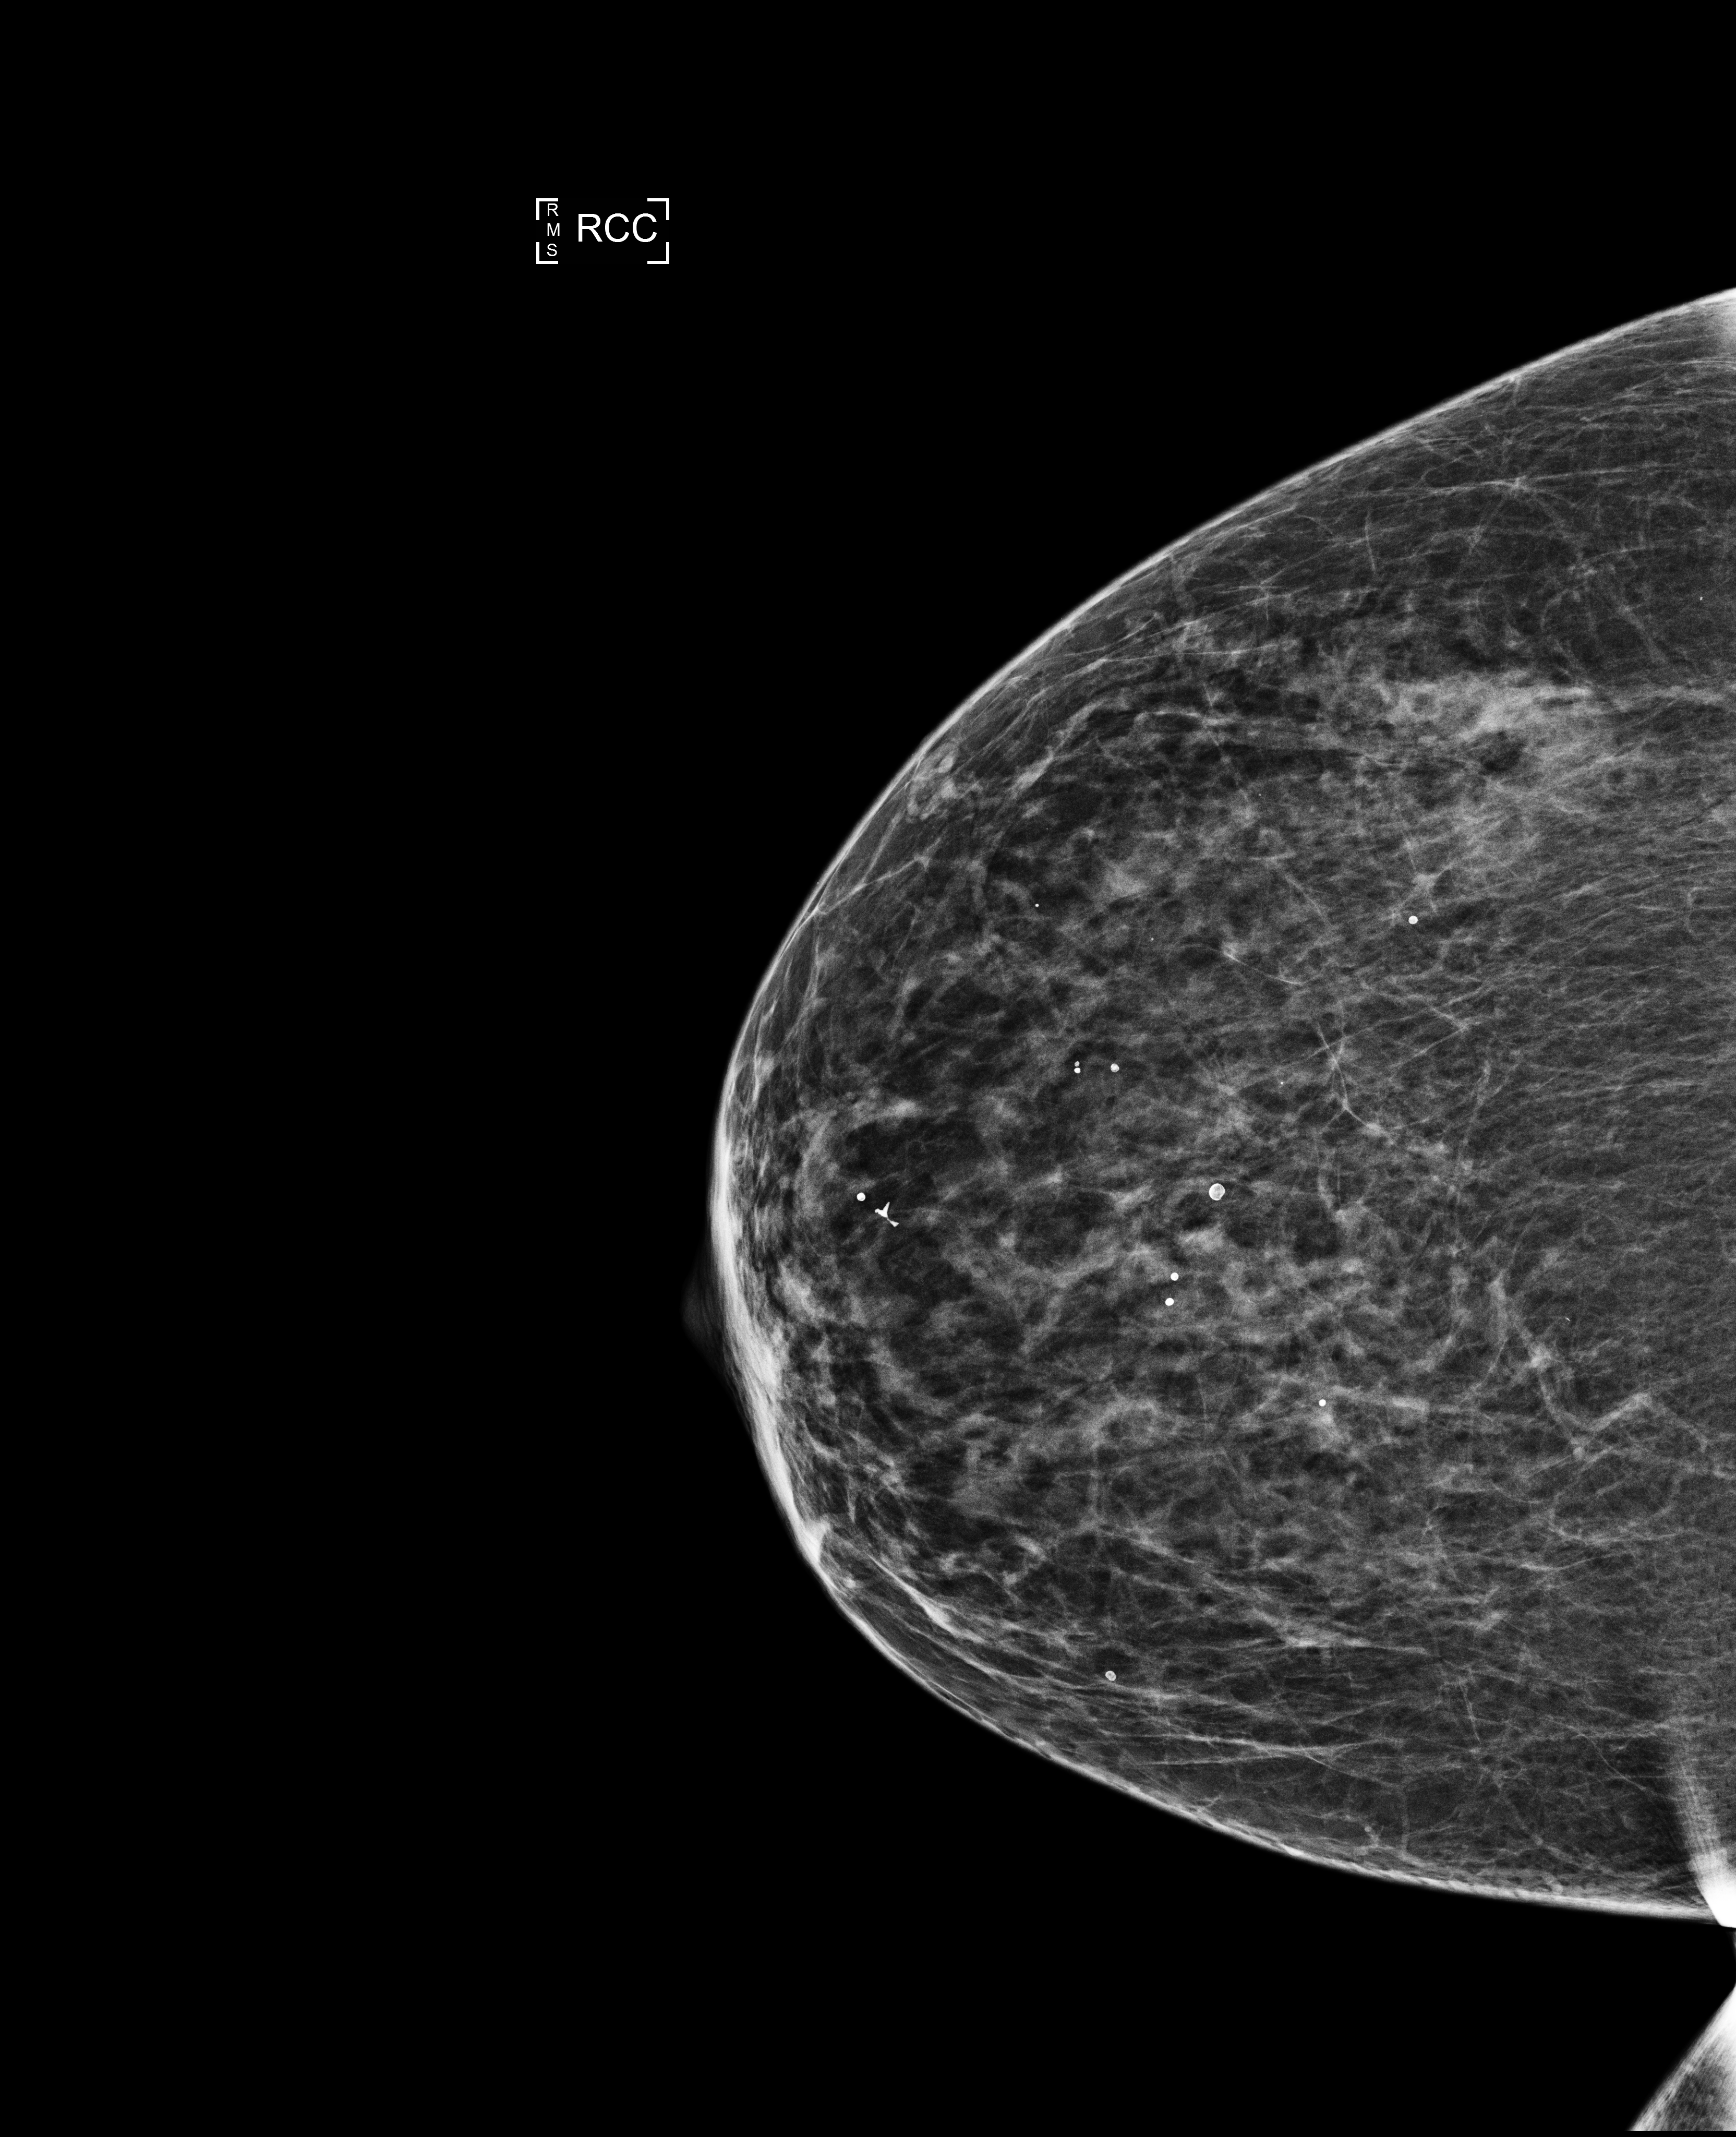
Full-field digital mammogram (FFDM); right breast; cranio-caudal projection; screening examination; compressed breast thickness 39 mm. Patient: female, 68 years.
Breast density at the screening exam (both breasts): heterogeneously dense (BI-RADS density category c). Final BI-RADS assessment for this screening round (tomosynthesis exam, both breasts): category 1. Recall: no recall after this screen.